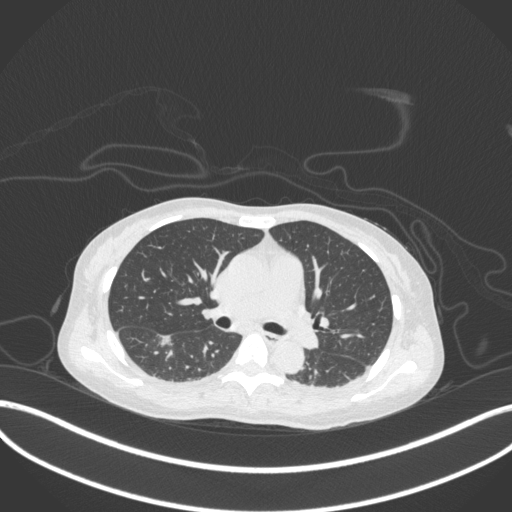
Chest CT, one axial slice; position 183 of 260 along the scan axis; reconstruction kernel B31f; lung window (W 1500 / L -600 HU); 1 mm slice thickness; 512 × 512 image matrix. Female patient, age 44 years. From the clinical record (not read from this slice): clinical TNM (as recorded): T1c N0 M0.
Structures marked on this image (rectangle marked by the reading radiologist):
- lung tumour (recorded histology: adenocarcinoma): bounding box <154,334,180,353> (left, top, right, bottom; pixels)